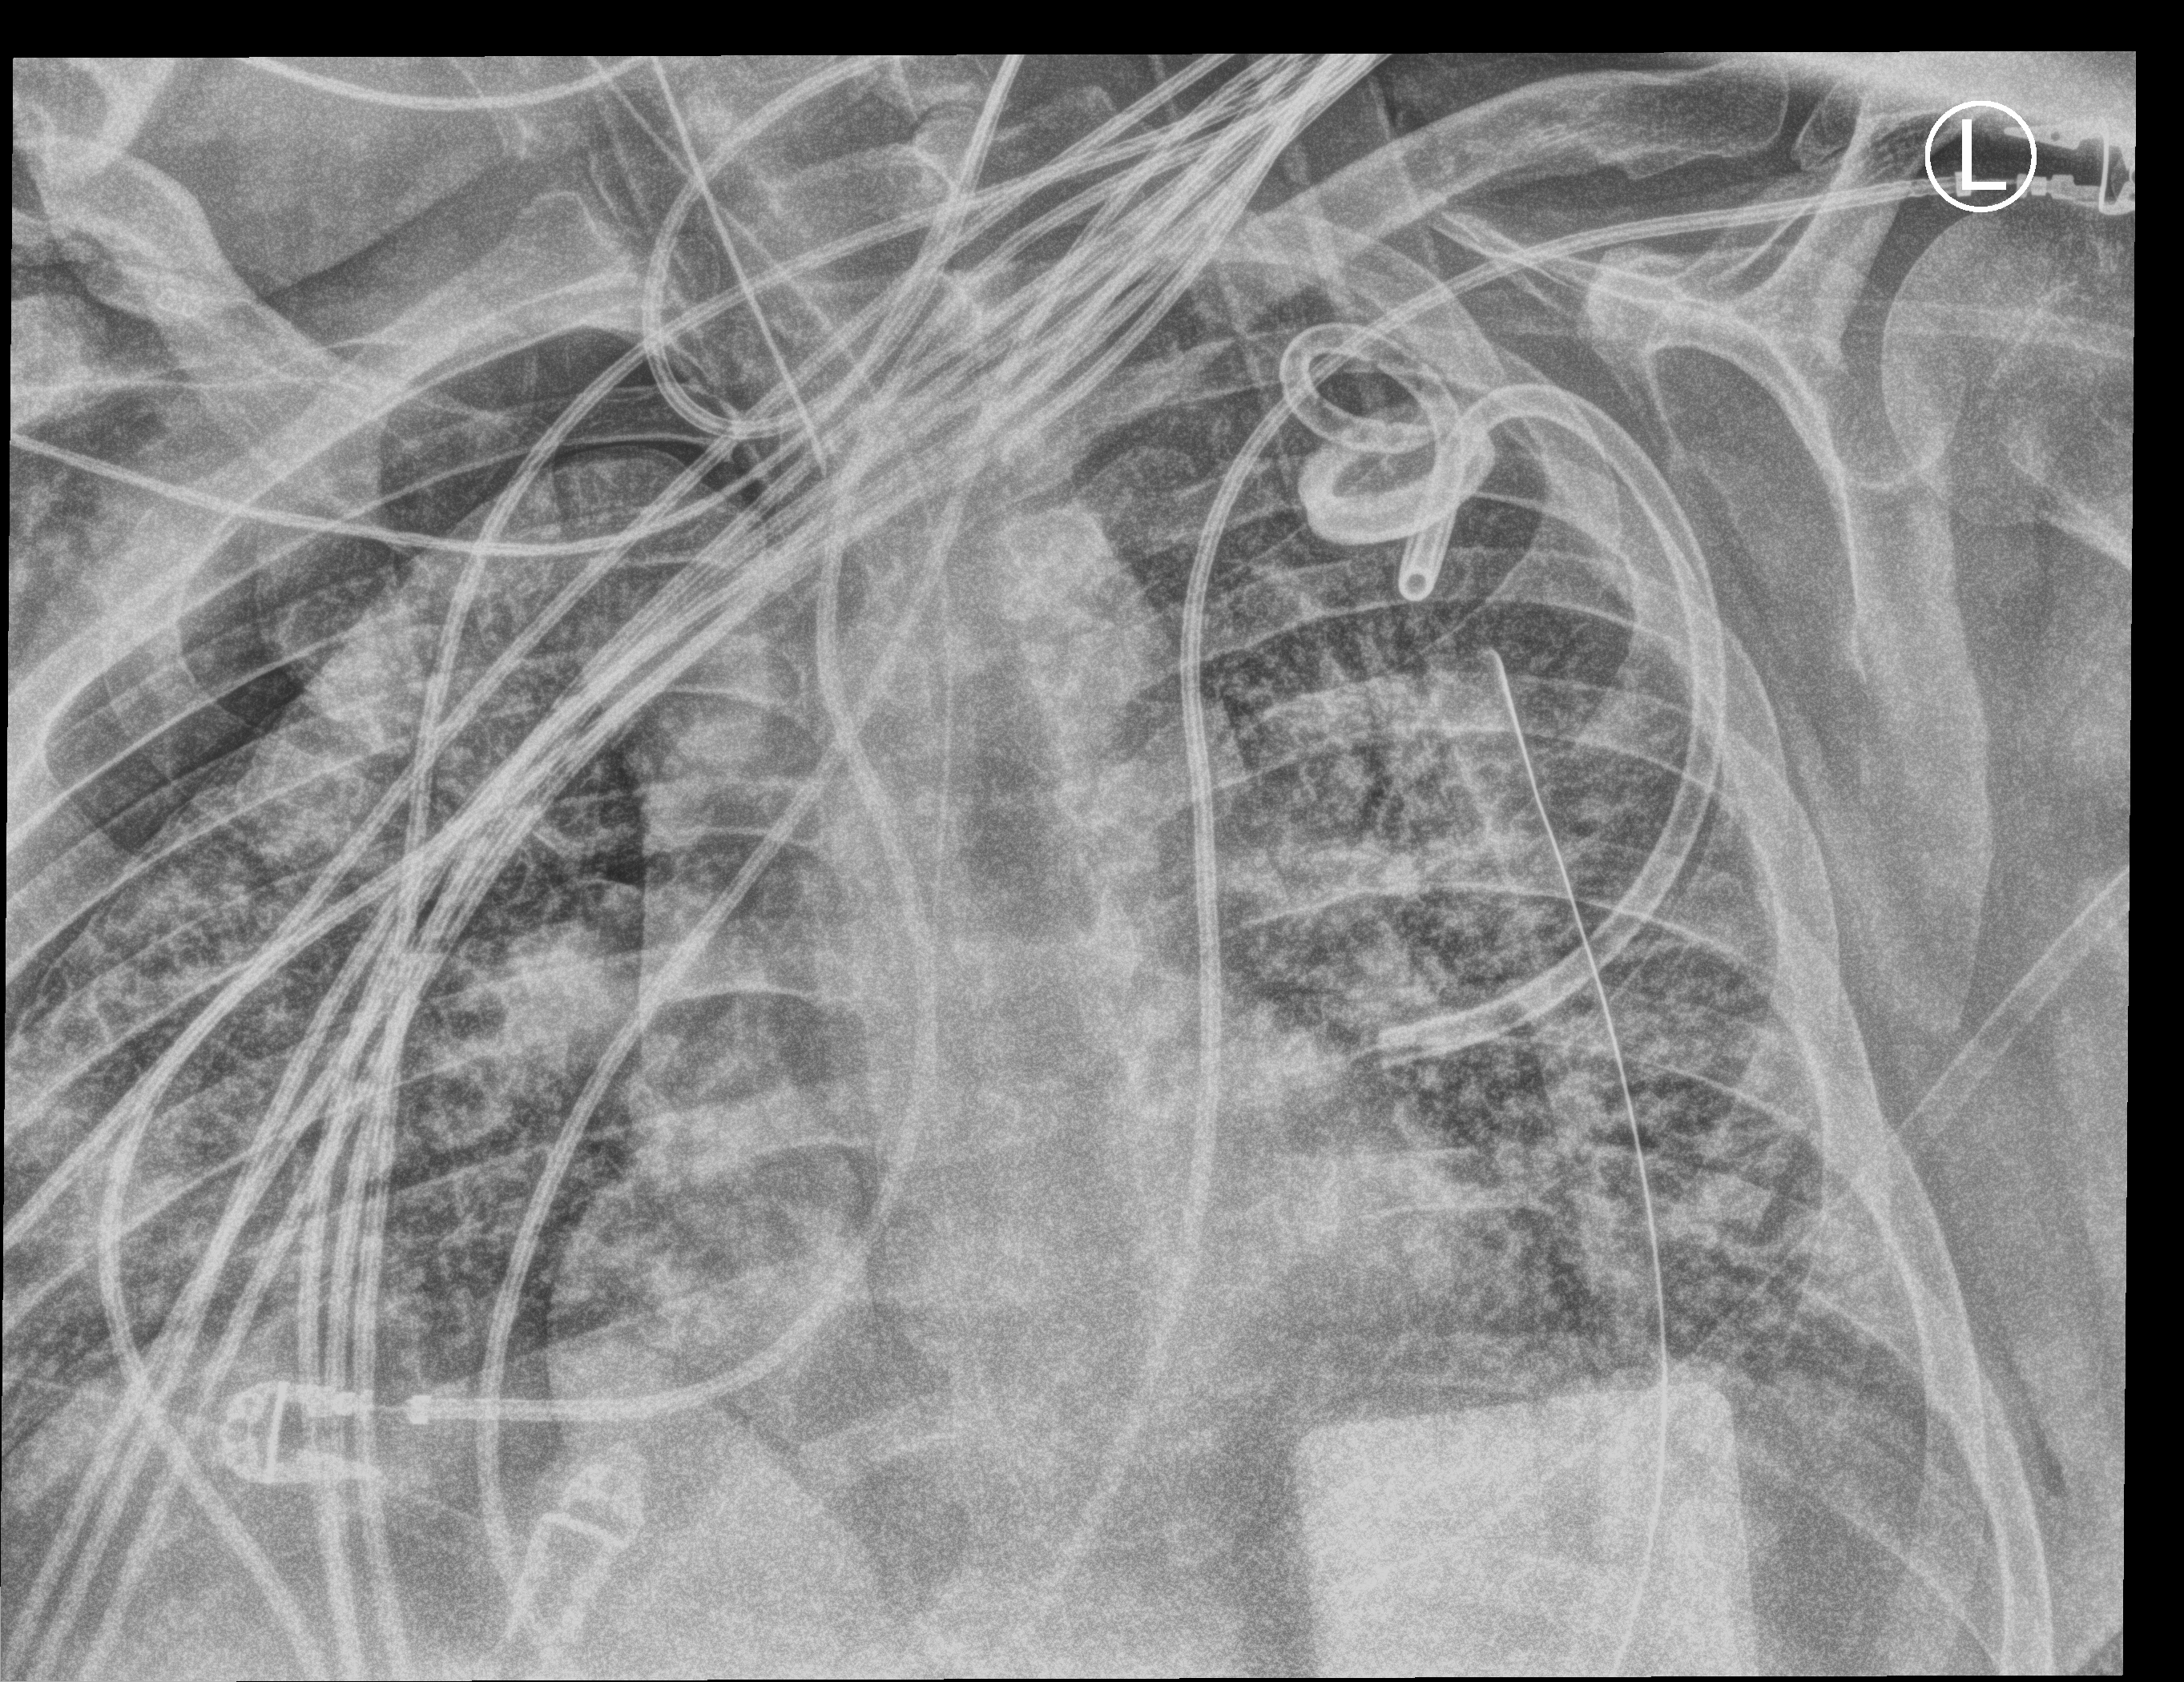
Portable chest radiograph. Adult patient hospitalised with COVID-19, age 18–59 years.
Hospital-stay facts (about this admission, not read from this image; timing relative to this image not recorded):
- mechanically ventilated during this hospital stay: yes